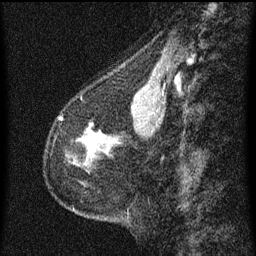
Breast MRI (dynamic contrast-enhanced), one sagittal slice. Position 23 of 60 along the scan axis. Dynamic contrast-enhanced series, image 2 of 3 at this slice position (ordered by acquisition). 1.5 T. TE 4.2 ms, TR 8 ms. 2 mm slice thickness. 256 × 256 image matrix. Female patient, age 56 years.
Structures marked on this image (semi-automatic segmentation, software-assisted and operator-edited):
- analysis volume of interest (the breast-tissue region the enhancement analysis was run in; not a lesion): box from (x=70, y=118) to (x=102, y=181) px
- tumour enhancement mask (voxels above the 70 % enhancement threshold inside the analysis volume of interest): (x=85, y=138)–(x=99, y=150)